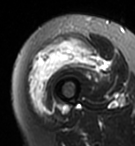
MRI of an extremity soft-tissue mass, one axial slice; slice 25 of 95 in the series (ordered by position); T2-weighted fat-saturated; MR volume resampled by the dataset authors to the PET/CT grid (not the native acquisition matrix); 3.27 mm slice thickness; 135 × 146 image matrix, field of view 132 × 143 mm. Female patient. Case-level facts recorded for this patient, not image findings: histological type: pleiomorphic undifferentiated sarcoma; grade: high; site of the primary tumour: right quadricep.
Outlined on this slice (expert contour drawn on MRI and transferred to this co-registered scan by the dataset authors):
- gross tumour volume including surrounding oedema: bounding box (x1, y1, x2, y2) in pixels: (30, 38, 102, 112)